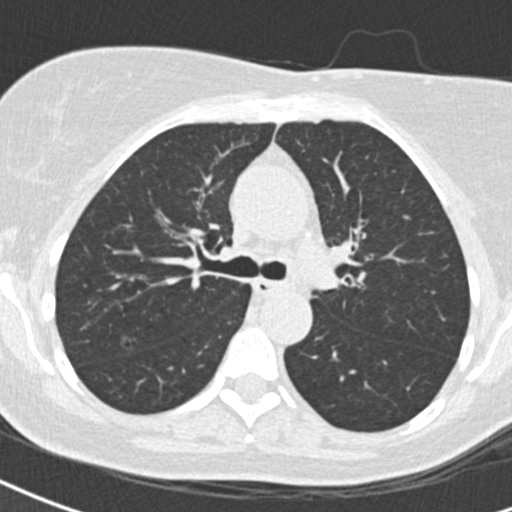
Axial slice from a low-dose chest CT screening exam; baseline screening round; lung window (W 1500 / L -600 HU); 2 mm slice thickness; standard (soft-tissue) reconstruction kernel (B30f); slice 63 of 184 in the series; 512 × 512 image matrix. Female, age 57 years at enrolment. Current smoker at enrolment.
Expert reader's lesion annotation, bounding box <112,332,140,357> (left, top, right, bottom; pixels). Screening reader's record for this exam (one nodule recorded; not confirmed to be the boxed lesion): non-calcified nodule or mass ≥4 mm, left upper lobe, 10 × 9 mm, spiculated (stellate) margins, soft tissue attenuation. Note: the box lies in the patient's right hemithorax on this image, whereas the reader's record names the left lung; they may be different findings. Official screen result: positive, change unspecified: nodule(s) >= 4 mm or enlarging nodule(s), mass(es), or other non-specific abnormalities suspicious for lung cancer. Later outcome: lung cancer diagnosed 153 days after this screen — non-small cell carcinoma, right upper lobe, stage IA (AJCC 6th edition), 13 mm at pathology.